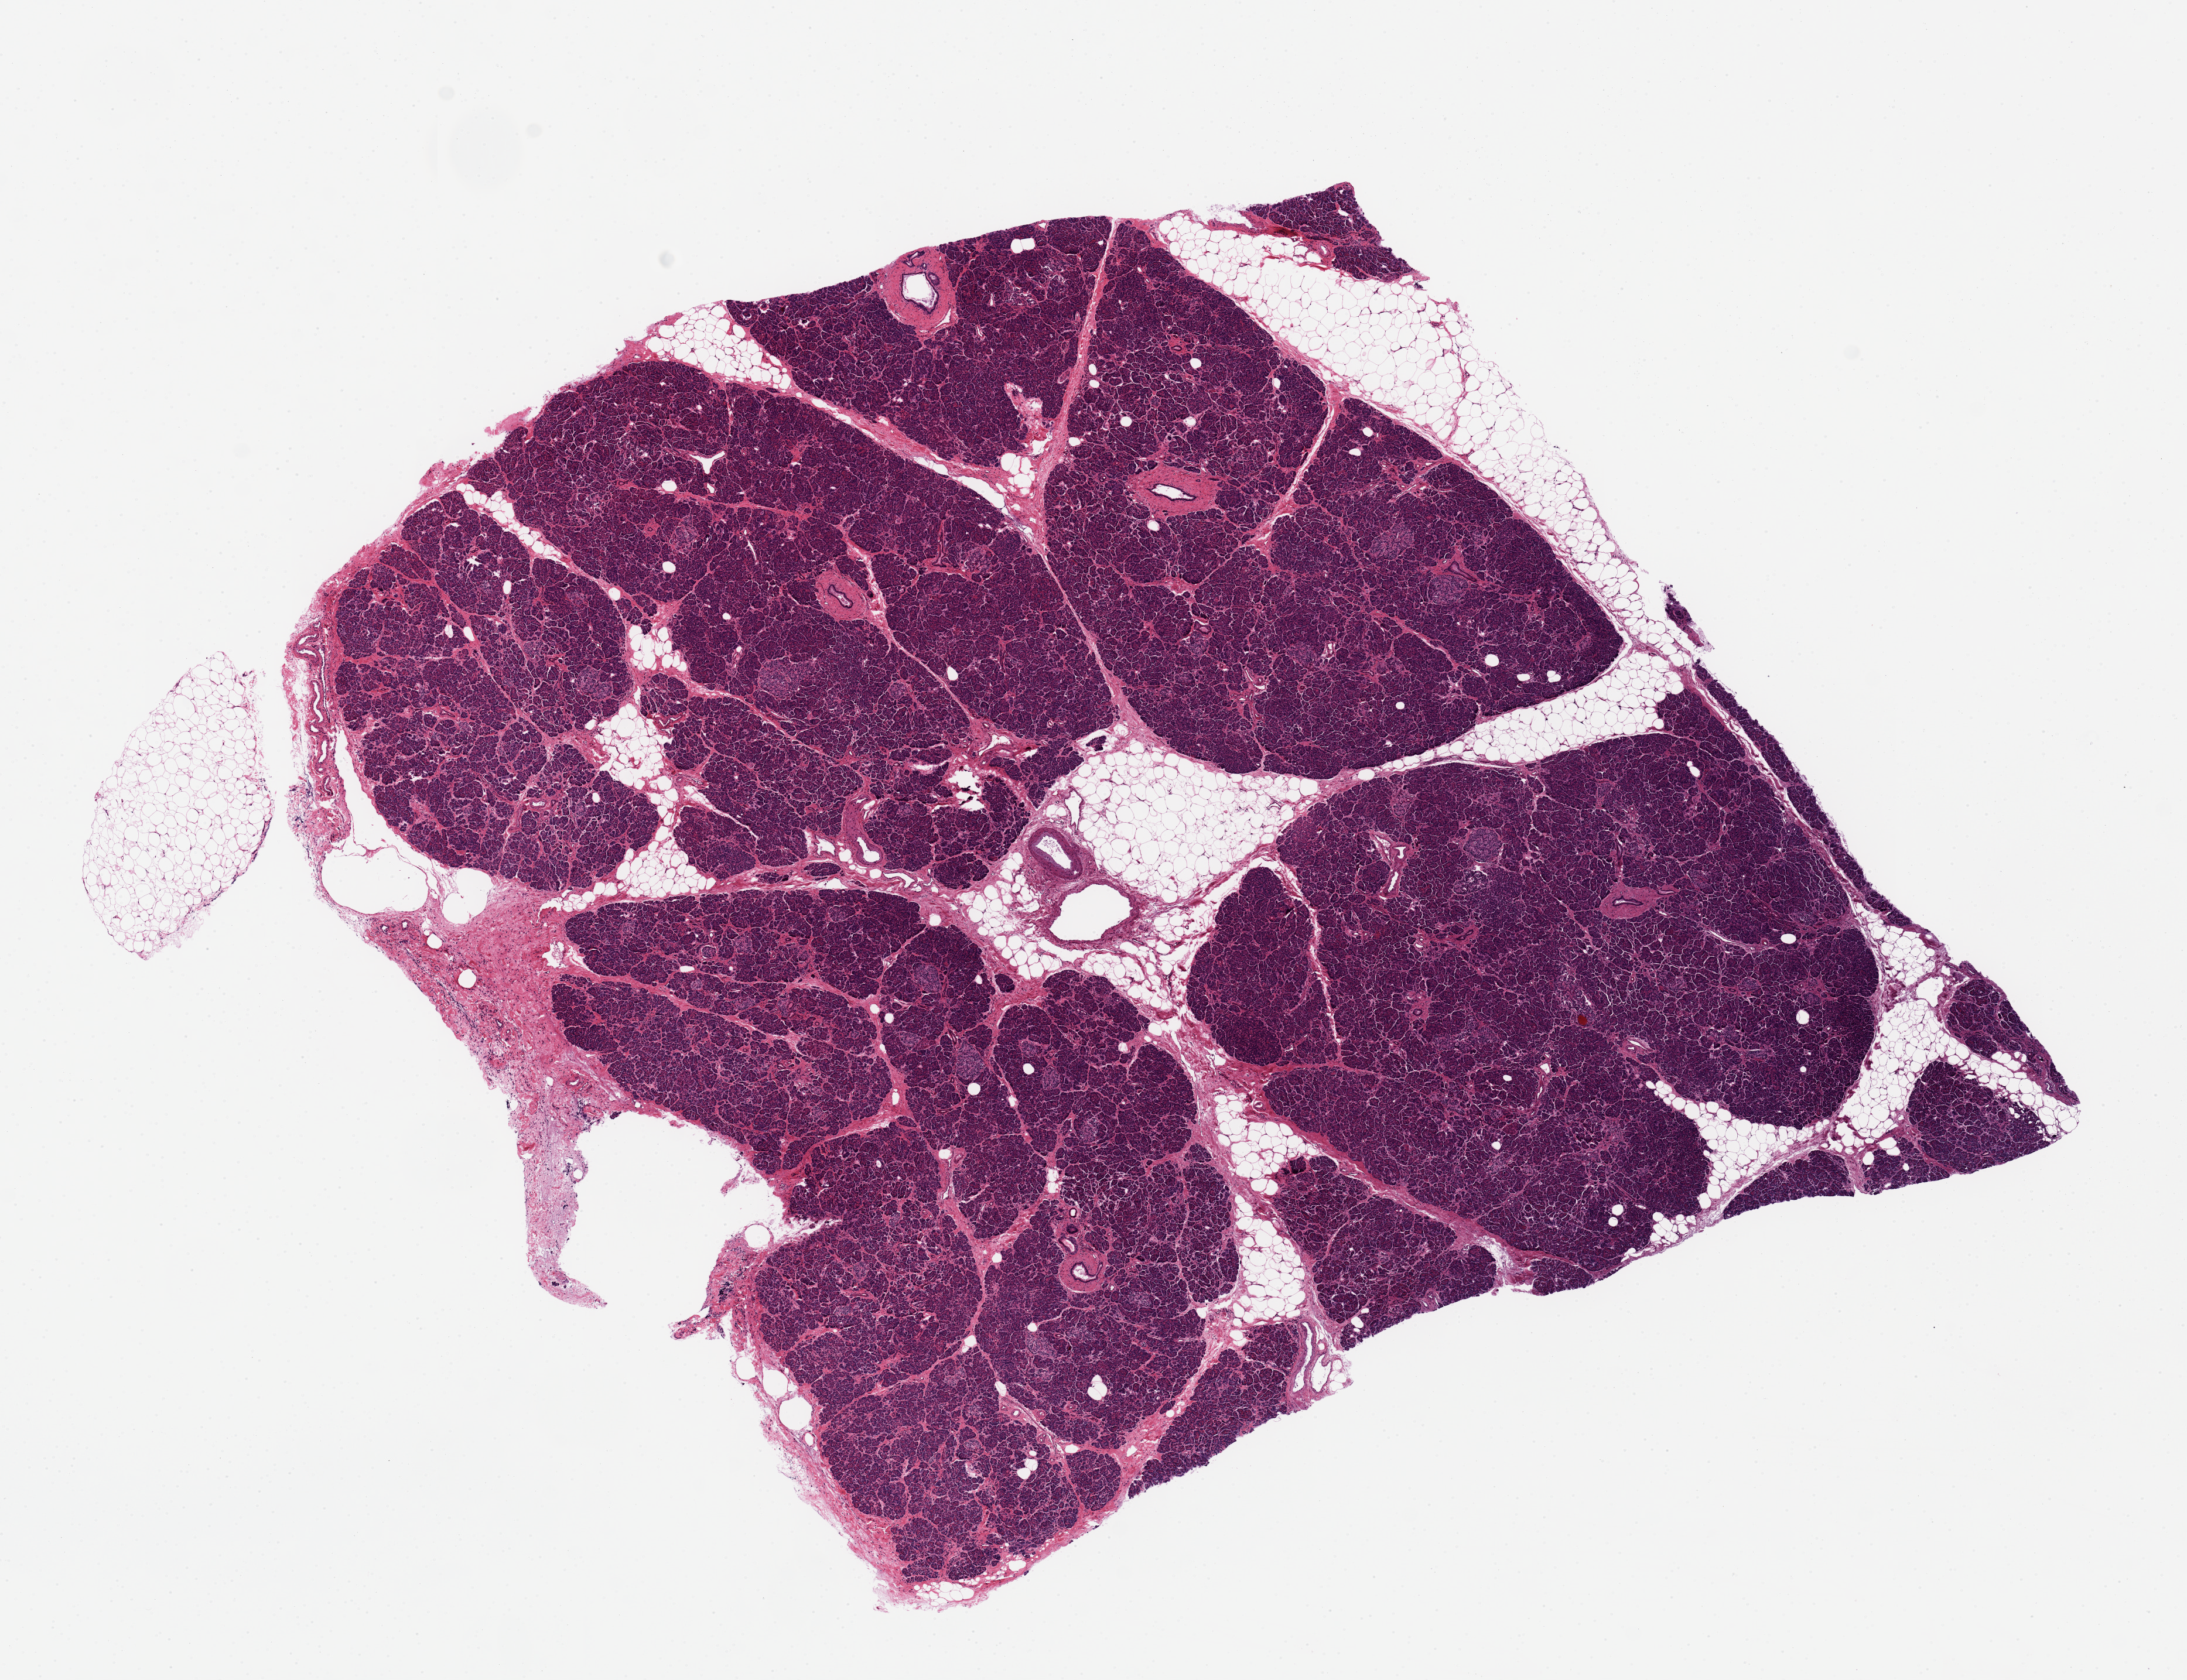
Hematoxylin and eosin (H&E) whole-slide image, brightfield, a low-resolution overview of the entire scanned area, about 14.8 x 11.3 mm (acquisition: 20x scan); PAXgene-fixed paraffin-embedded (PFPE) section; target tissue: pancreas; tissue donor sample. Male donor.
• pathologist's review note for this sample: 90% parenchyma, 10% fat. Remarkably well-preserved; numerous islets of Langherhans noted